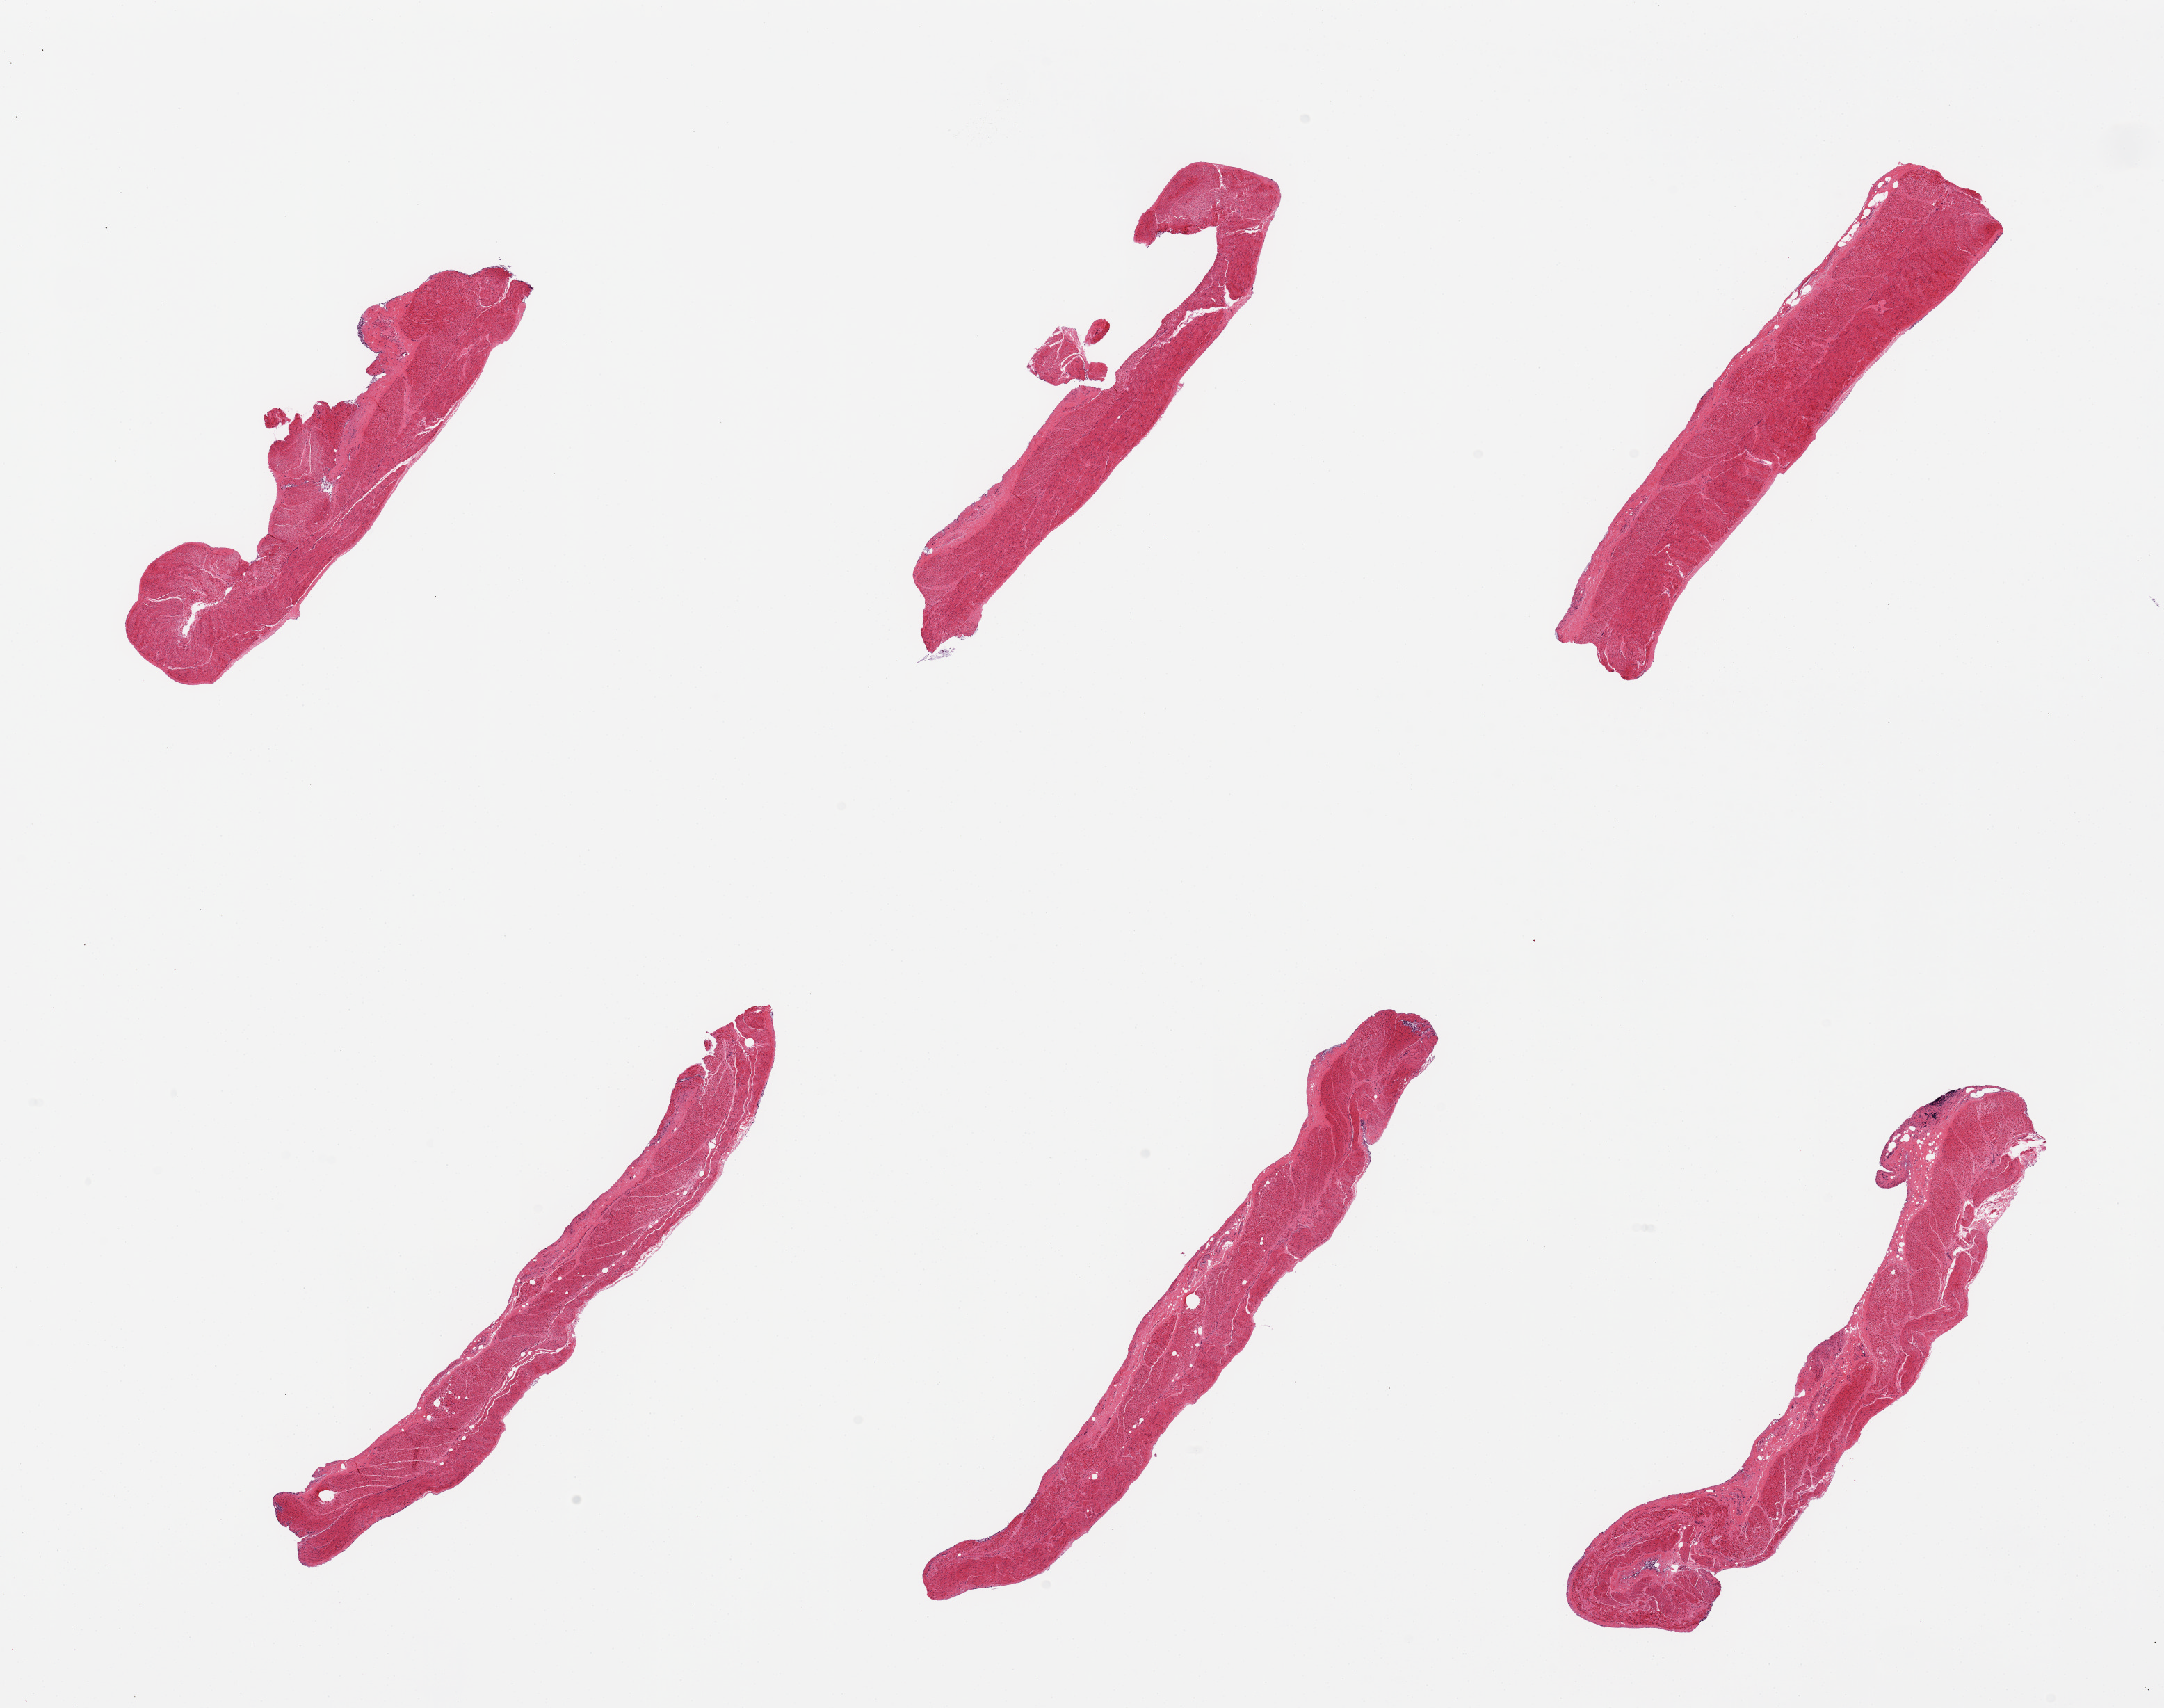
Whole-slide image, haematoxylin and eosin stain, brightfield, shown as a low-resolution overview of the whole scanned area (about 24.6 x 19.4 mm, from a 20x scan). PAXgene-fixed paraffin-embedded (PFPE) section. Target tissue: sigmoid colon. Tissue donor sample.
Review note (as recorded): 6 pieces.